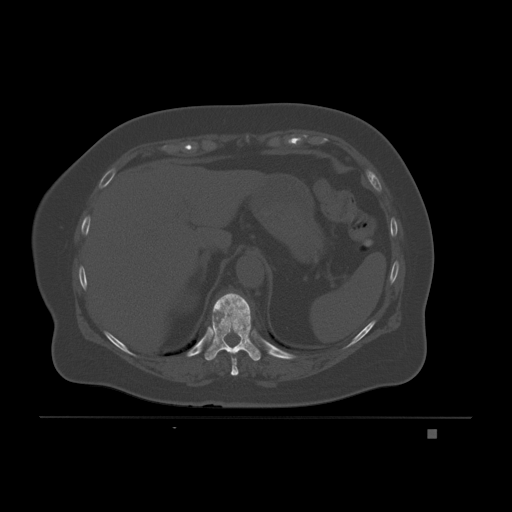
CT including the spine, one axial slice. Position 101 of 221 along the scan axis. Bone window (W 1800 / L 400 HU). 512 × 512 image matrix, field of view 474 × 474 mm. Female patient, age 63 years. Case-level facts recorded for this patient, not image findings: primary cancer: breast.
Structures marked on this image (semi-automatic segmentation, software-assisted and operator-edited):
- T10 vertebra: box from (x=204, y=293) to (x=261, y=361) px
- T9 vertebra: (x=231, y=357)–(x=239, y=376)